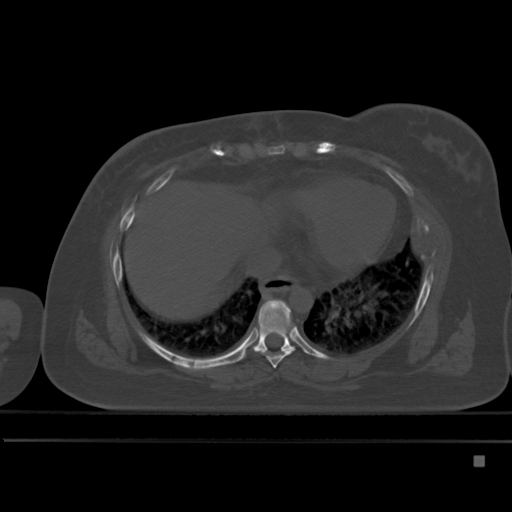
CT including the spine, one axial slice. Position 284 of 495 along the scan axis. Bone window (W 1800 / L 400 HU). 1.5 mm slice thickness. 512 × 512 image matrix. Female patient, age 33 years. Case-level facts recorded for this patient, not image findings: primary cancer: breast; vertebrae with lytic lesions (as recorded): T1.
Annotated regions visible in this slice (semi-automatic segmentation, software-assisted and operator-edited):
- T7 vertebra: bounding box <266,303,296,368> (left, top, right, bottom; pixels)
- T8 vertebra: <237,299,295,360>